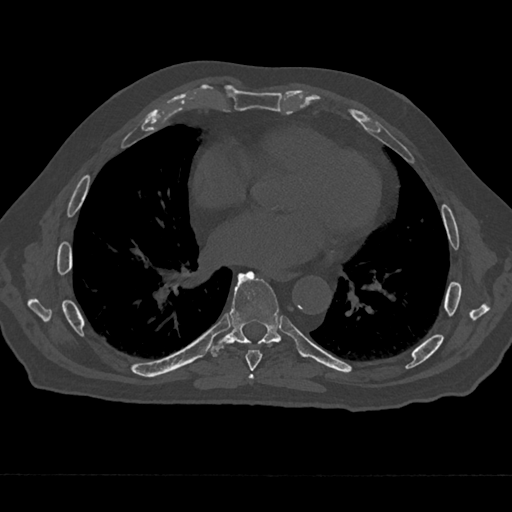
CT including the spine, one axial slice. Slice 340 of 797 in the series (ordered by position). Reconstruction kernel Br40s/3. 120 kVp. Bone window (W 1800 / L 400 HU). 0.5 mm slice thickness. 512 × 512 image matrix, field of view 377 × 377 mm. Male patient, age 75 years. Case-level facts recorded for this patient, not image findings: primary cancer: renal.
Structures marked on this image (semi-automatic segmentation, software-assisted and operator-edited):
- T6 vertebra: bounding box [x1, y1, x2, y2] px = [249, 374, 254, 380]
- T7 vertebra: [243, 343, 272, 371]
- T8 vertebra: [210, 271, 281, 355]